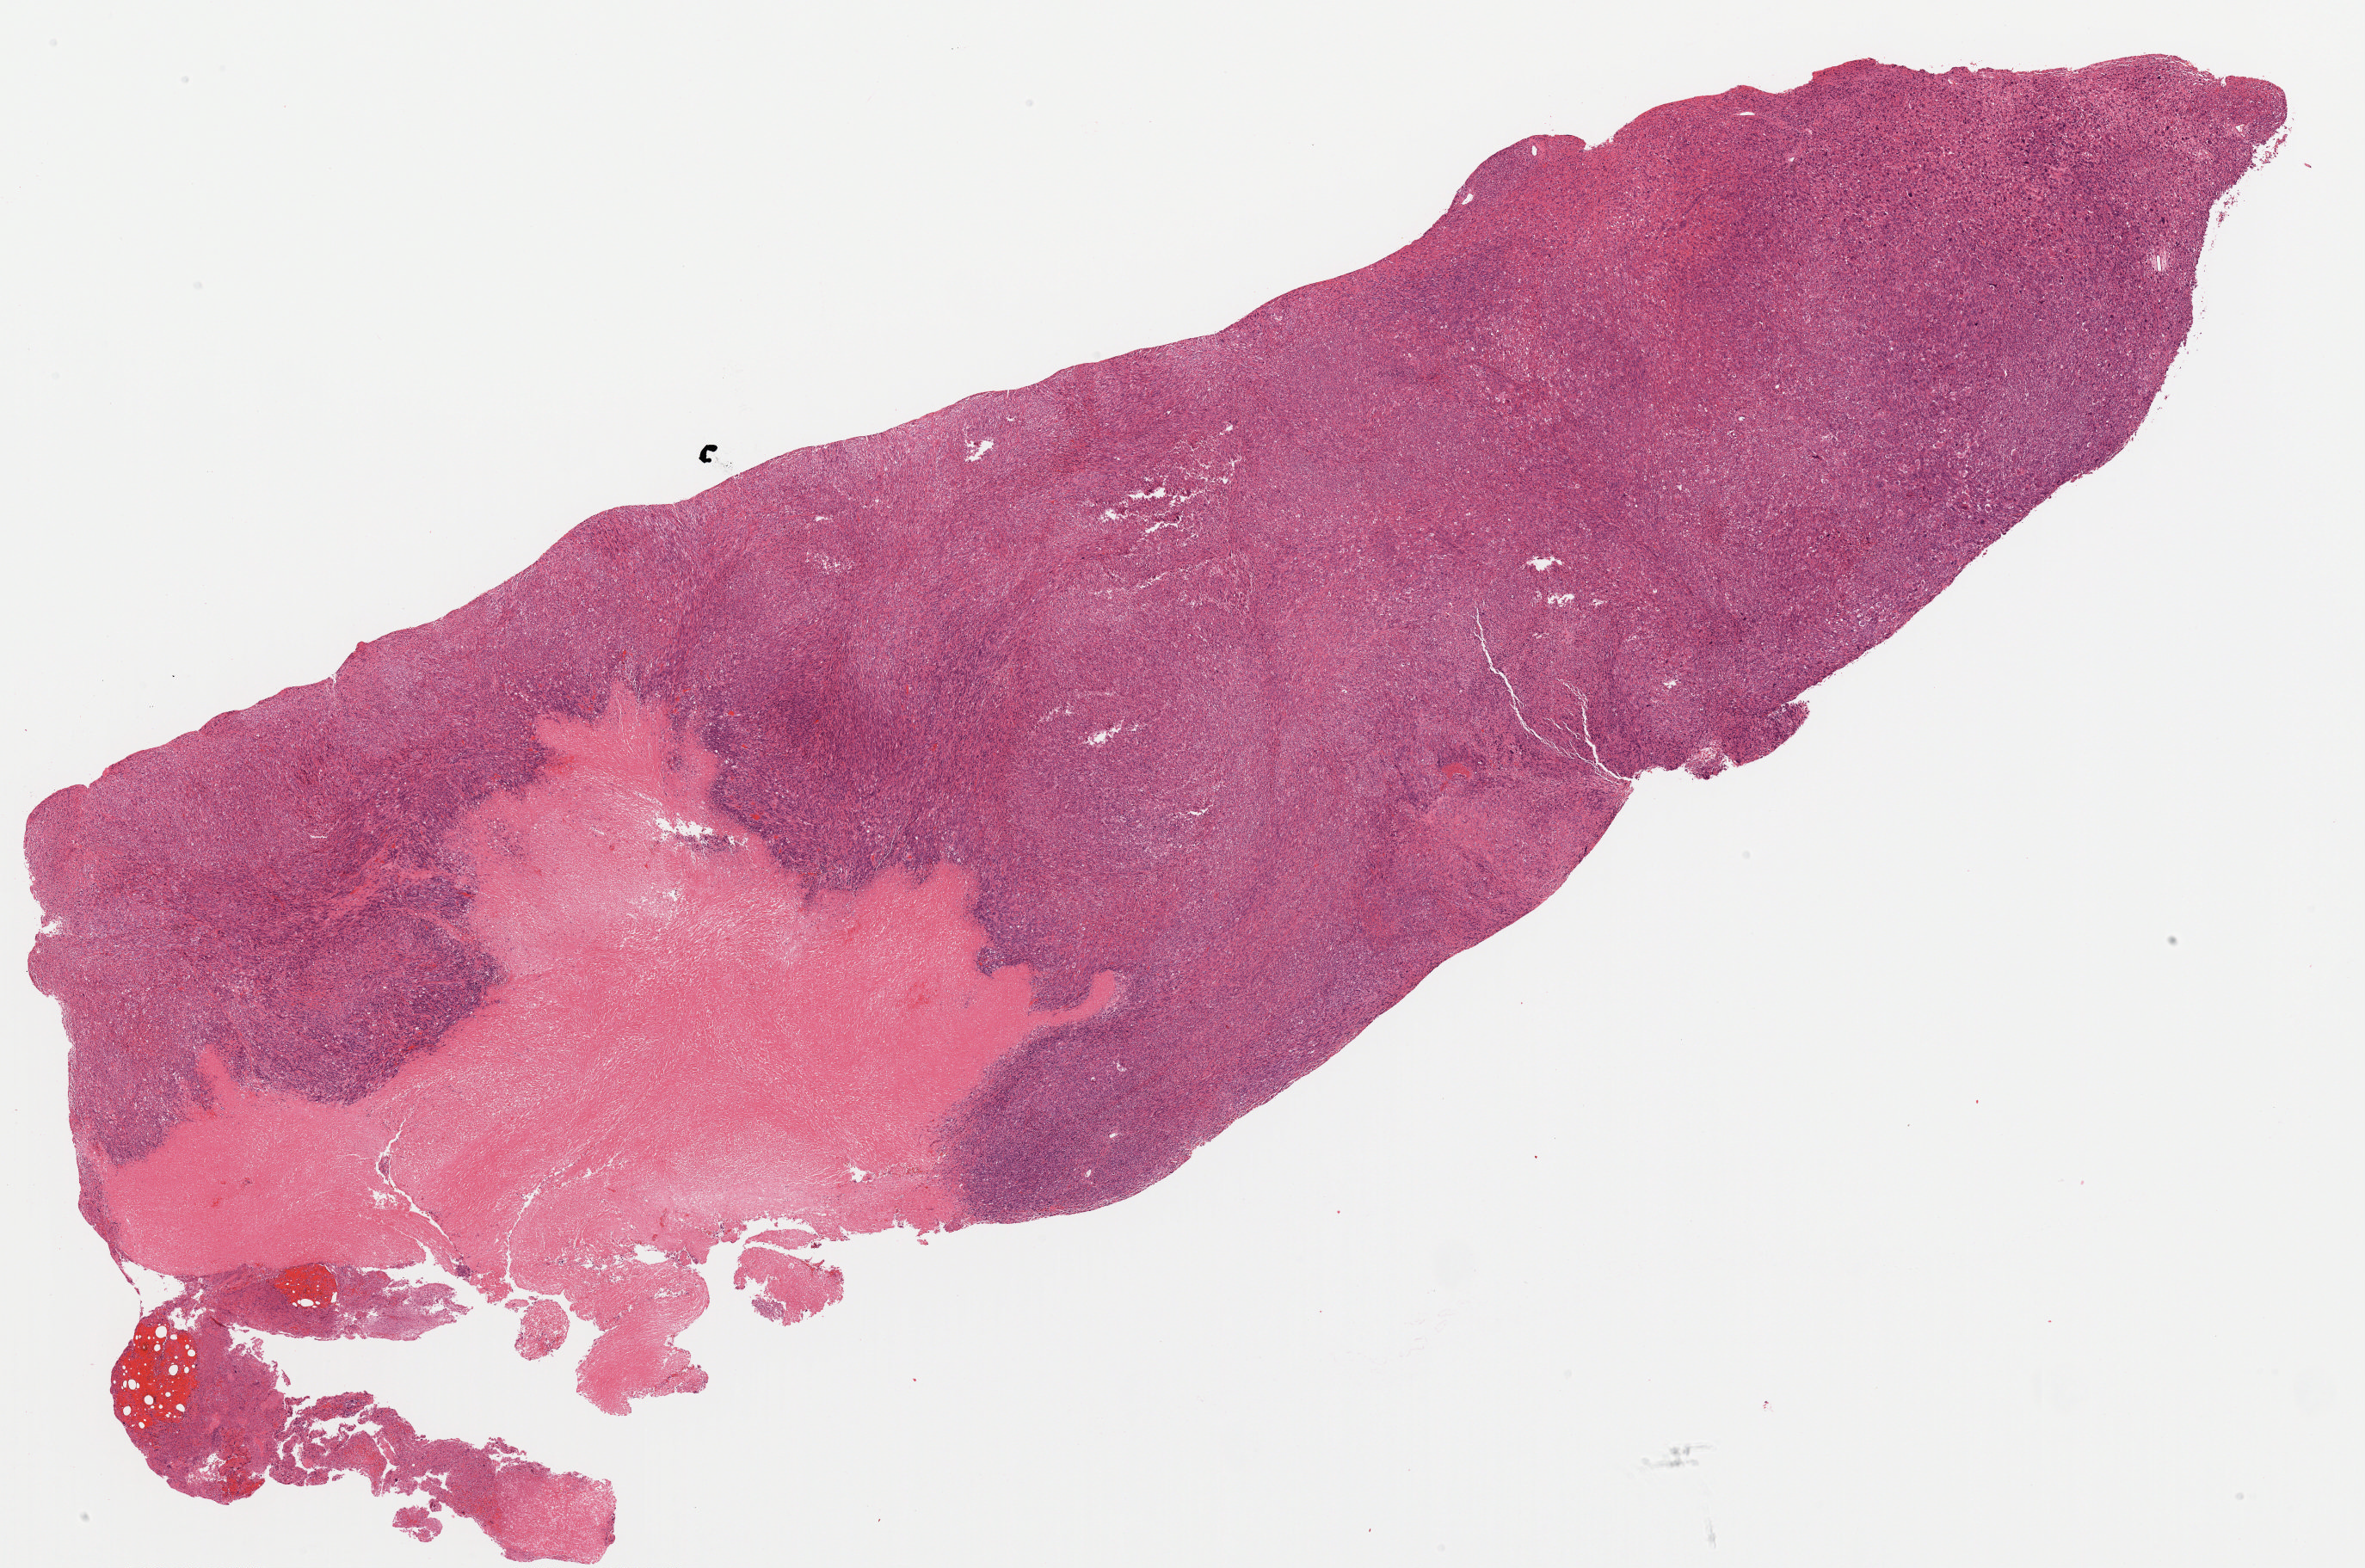
H&E whole-slide image — a low-resolution overview of the entire scanned area, about 22.0 x 14.6 mm (acquisition: 20x scan); formalin-fixed paraffin-embedded (FFPE) diagnostic section; primary tumour sample from the uterus. Patient: female, age at initial diagnosis 69 years.
Pathologic diagnosis: Leiomyosarcoma, NOS.